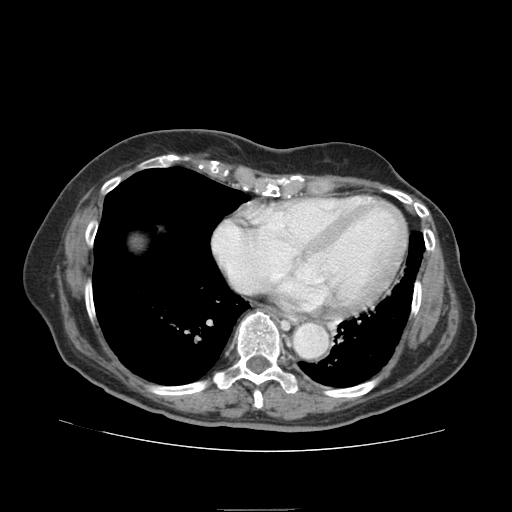
Contrast-enhanced abdominal CT (liver protocol), one axial slice; slice 82 of 95 in the series (ordered by position); reconstruction kernel STANDARD; 140 kVp; soft-tissue window (W 400 / L 40 HU); 2.5 mm slice thickness; 512 × 512 image matrix, field of view 360 × 360 mm. From the clinical record (not read from this slice): diagnosis: hepatocellular carcinoma (patient treated with transarterial chemoembolisation; whether this scan precedes or follows treatment is not stated here); TNM stage (as recorded): Stage-IVA; Child-Pugh class: B; tumour differentiation: moderately differentiated; tumour nodularity: uninodular.
Outlined on this slice (semi-automatic segmentation, software-assisted and operator-edited):
- abdominal aorta: bounding box (x1, y1, x2, y2) in pixels: (294, 323, 328, 358)
- liver parenchyma outside the tumour (the mass and vessels are separate outlines, so this box may not span the whole liver): (130, 234, 146, 250)